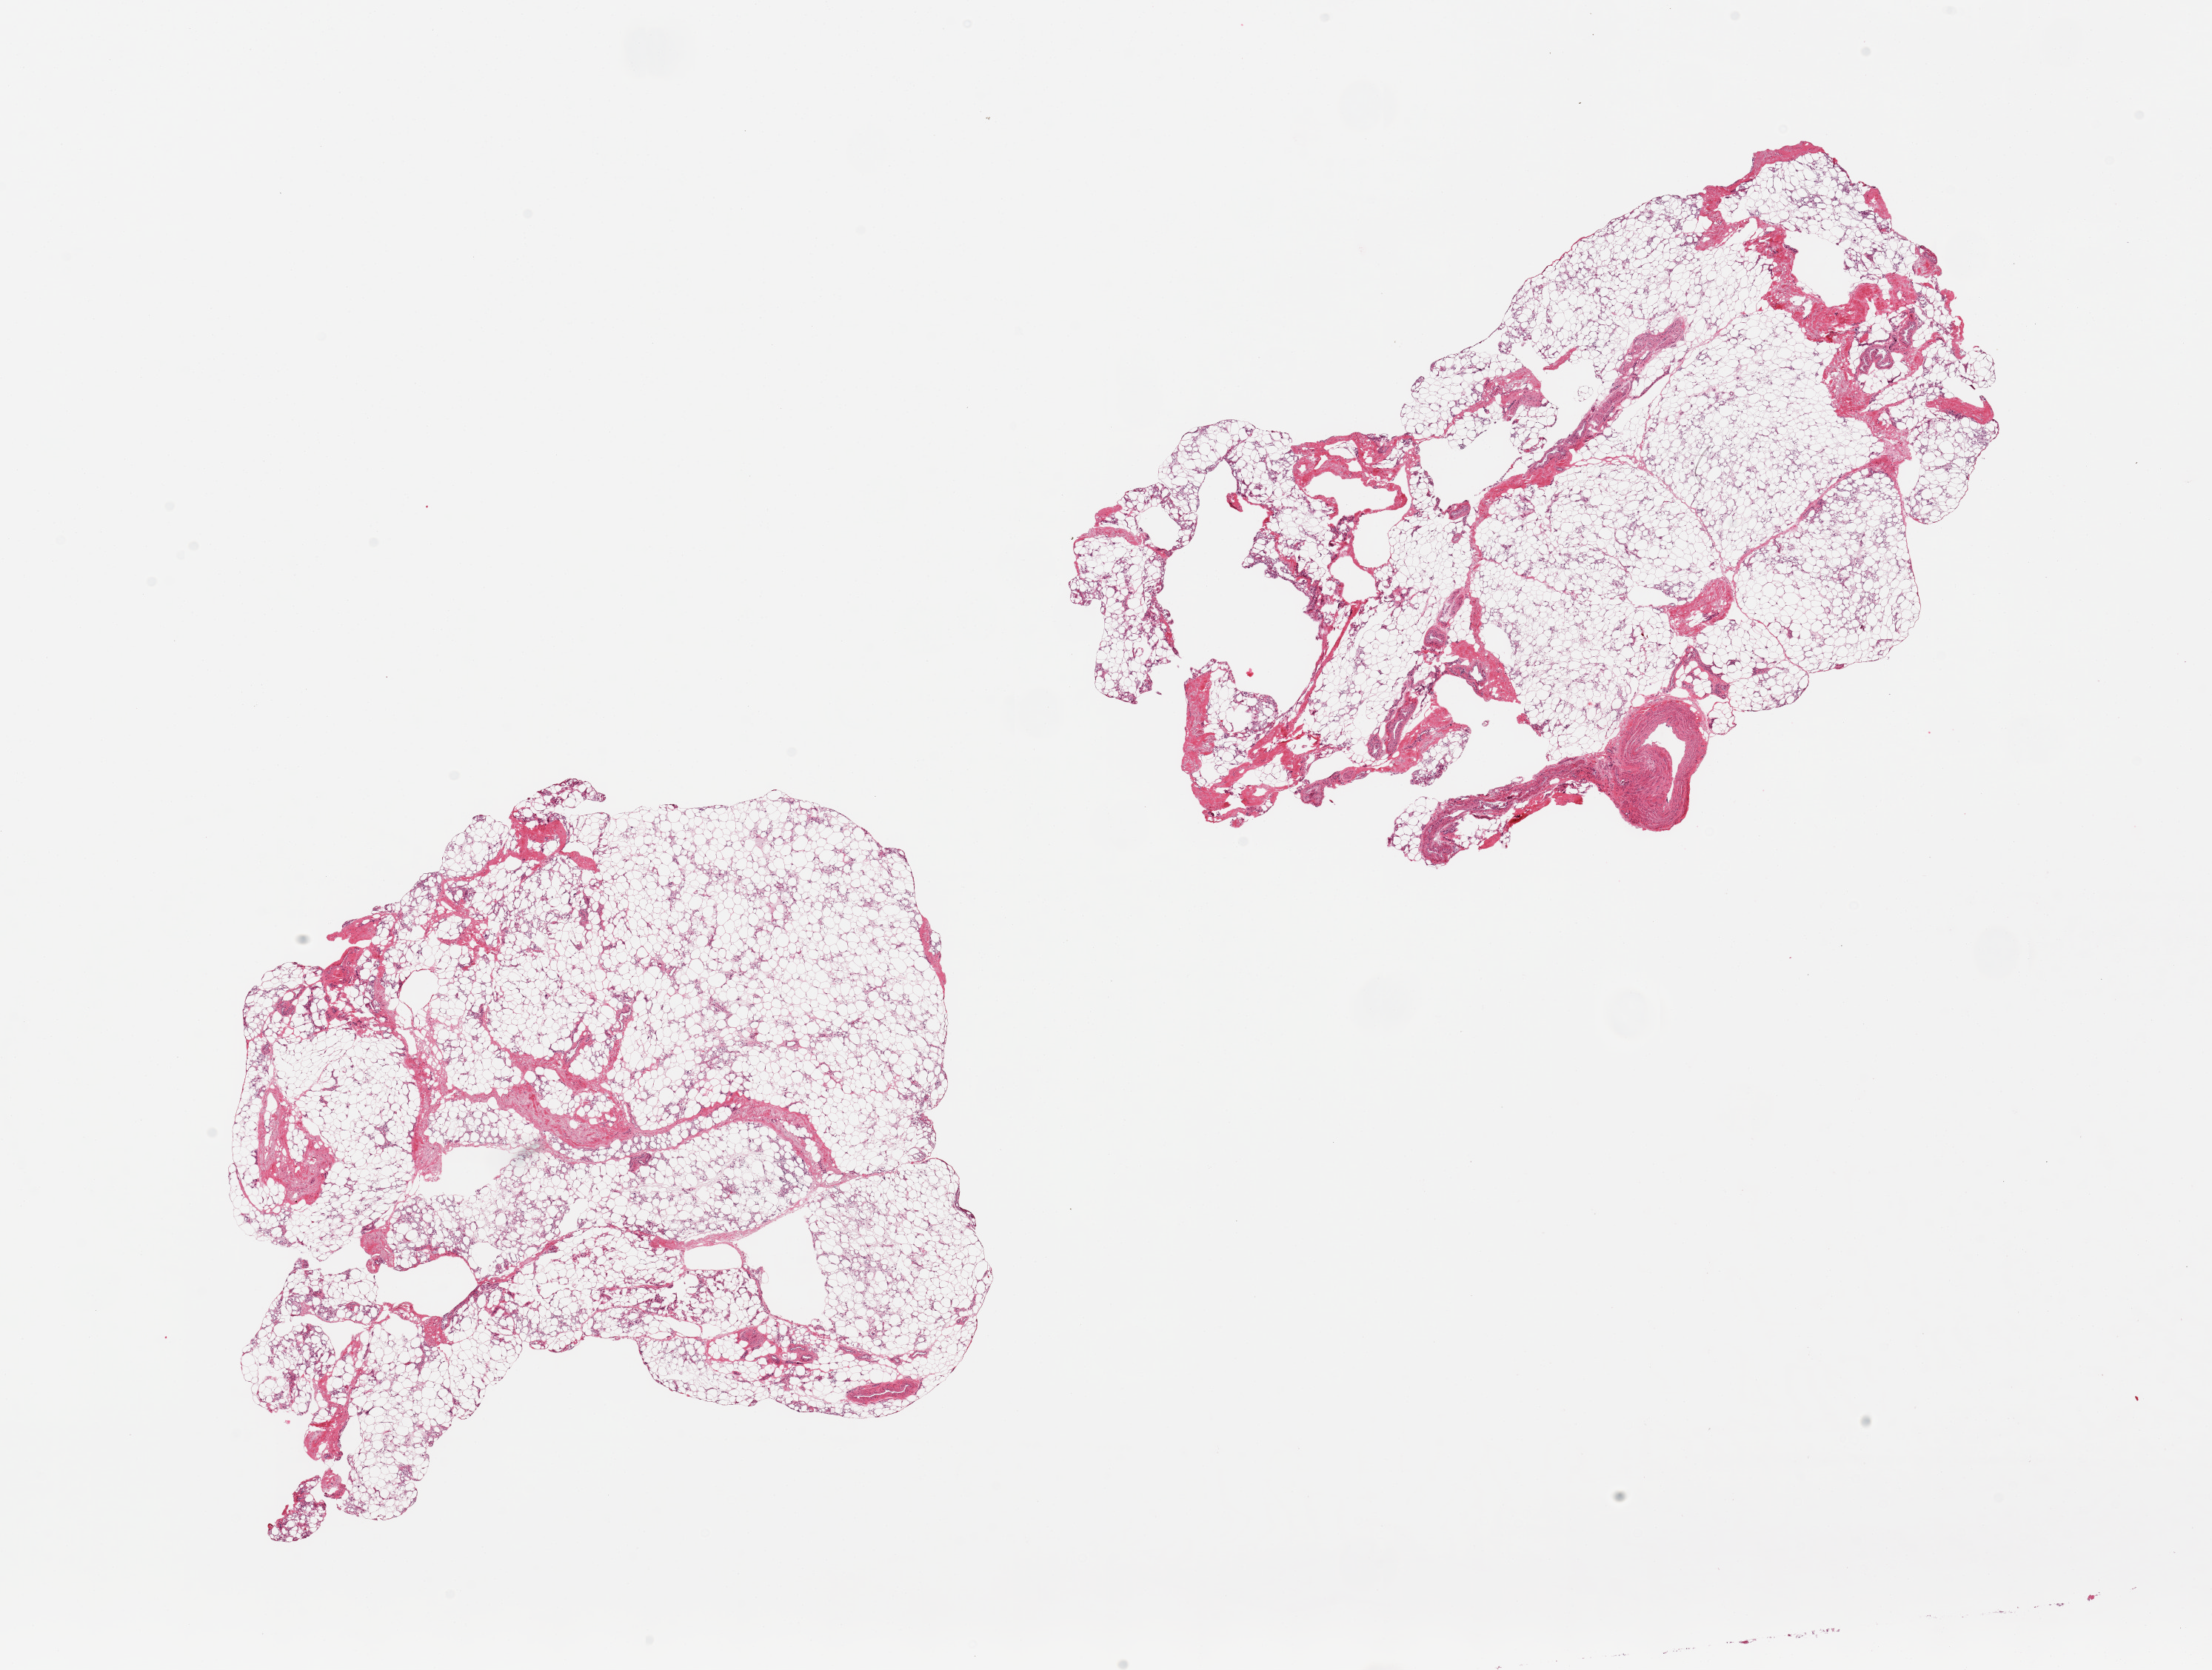
H&E whole-slide image, whole scanned area (about 23.6 x 17.8 mm) shown as a low-resolution overview. PAXgene-fixed paraffin-embedded (PFPE) section. Section of adipose tissue (target tissue). Donor tissue sample. Male donor.
• reviewer comment on this tissue sample: 2 pieces; <10% fibrous component